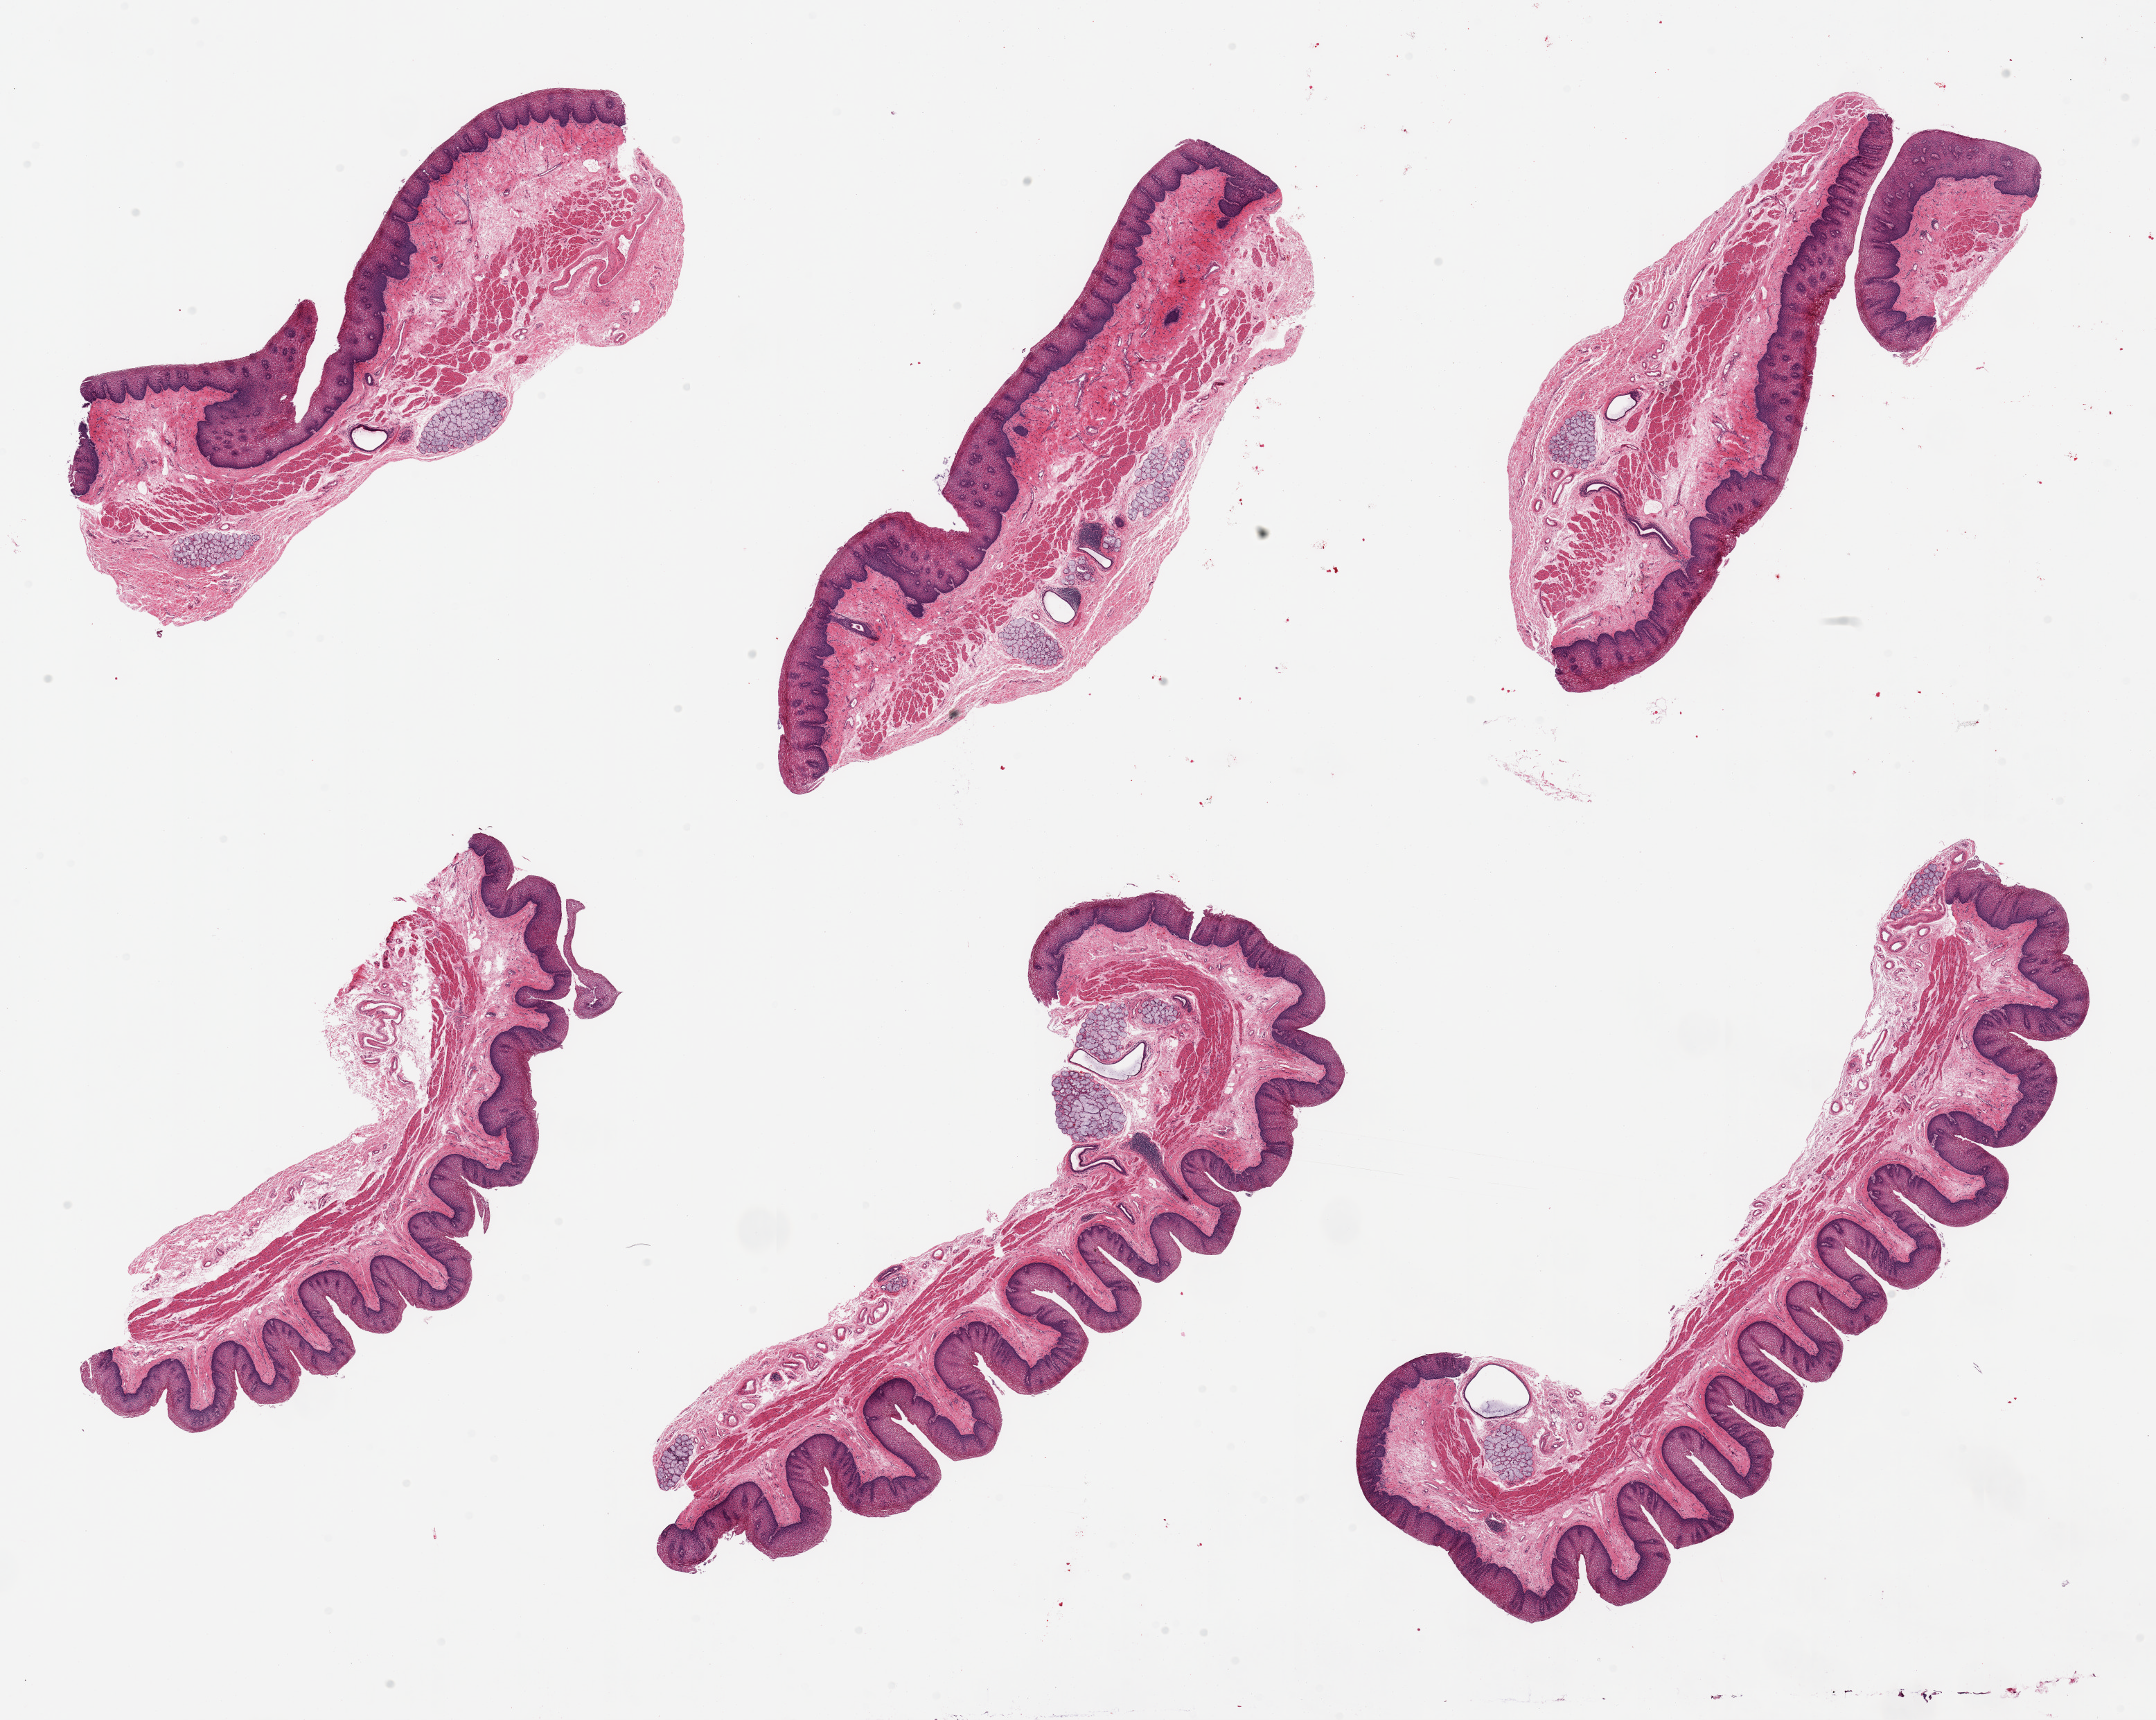
H&E whole-slide image — shown as a low-resolution overview of the whole scanned area (about 24.6 x 19.6 mm, slide scanned at 20x), PAXgene-fixed paraffin-embedded (PFPE) section, section of esophageal mucous membrane (target tissue), tissue donor sample.
• pathologist's review note for this sample: 6 pieces, well preserved; squamous mcuosa is ~0.3mm, 20-30% thickness; Submucosal mucus glands present